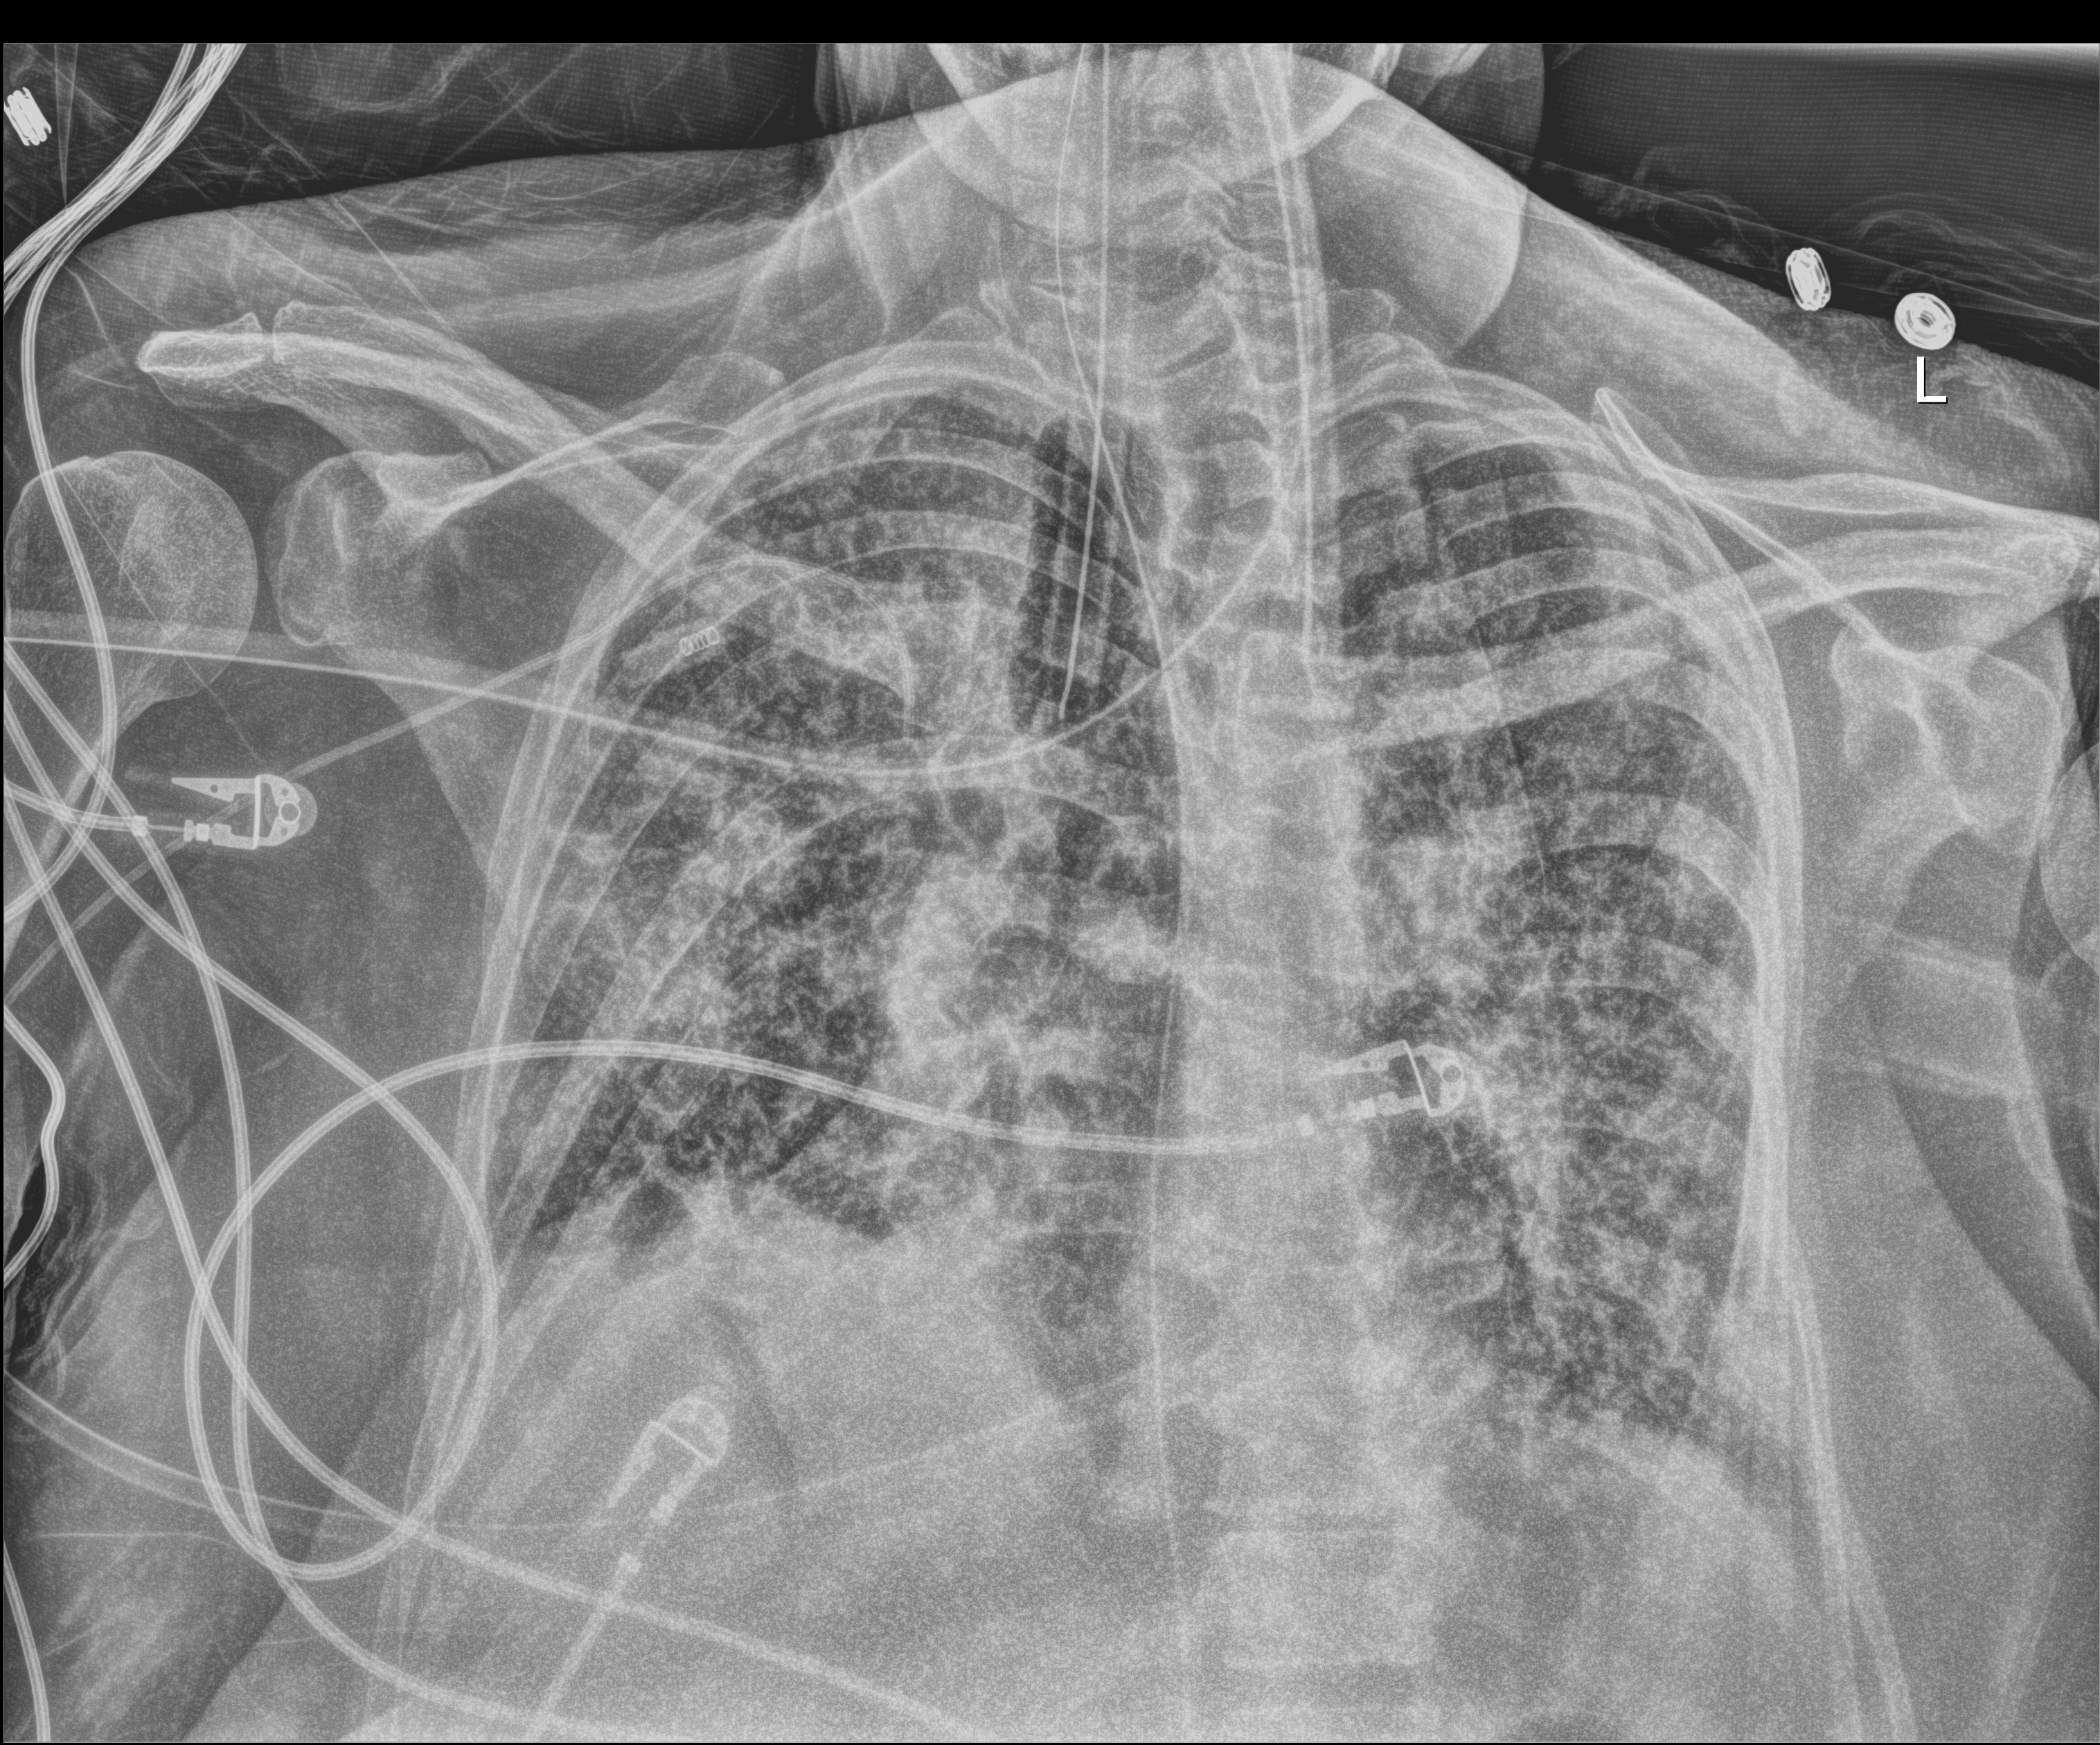
Bedside chest radiograph (digital radiography); anteroposterior (AP) projection. Patient hospitalised with COVID-19; female, aged 60–74 years.
Admission-level facts for this patient (not findings on this image; timing relative to this image not recorded):
- admitted to intensive care during this hospital stay: yes
- length of hospital stay: 45 days